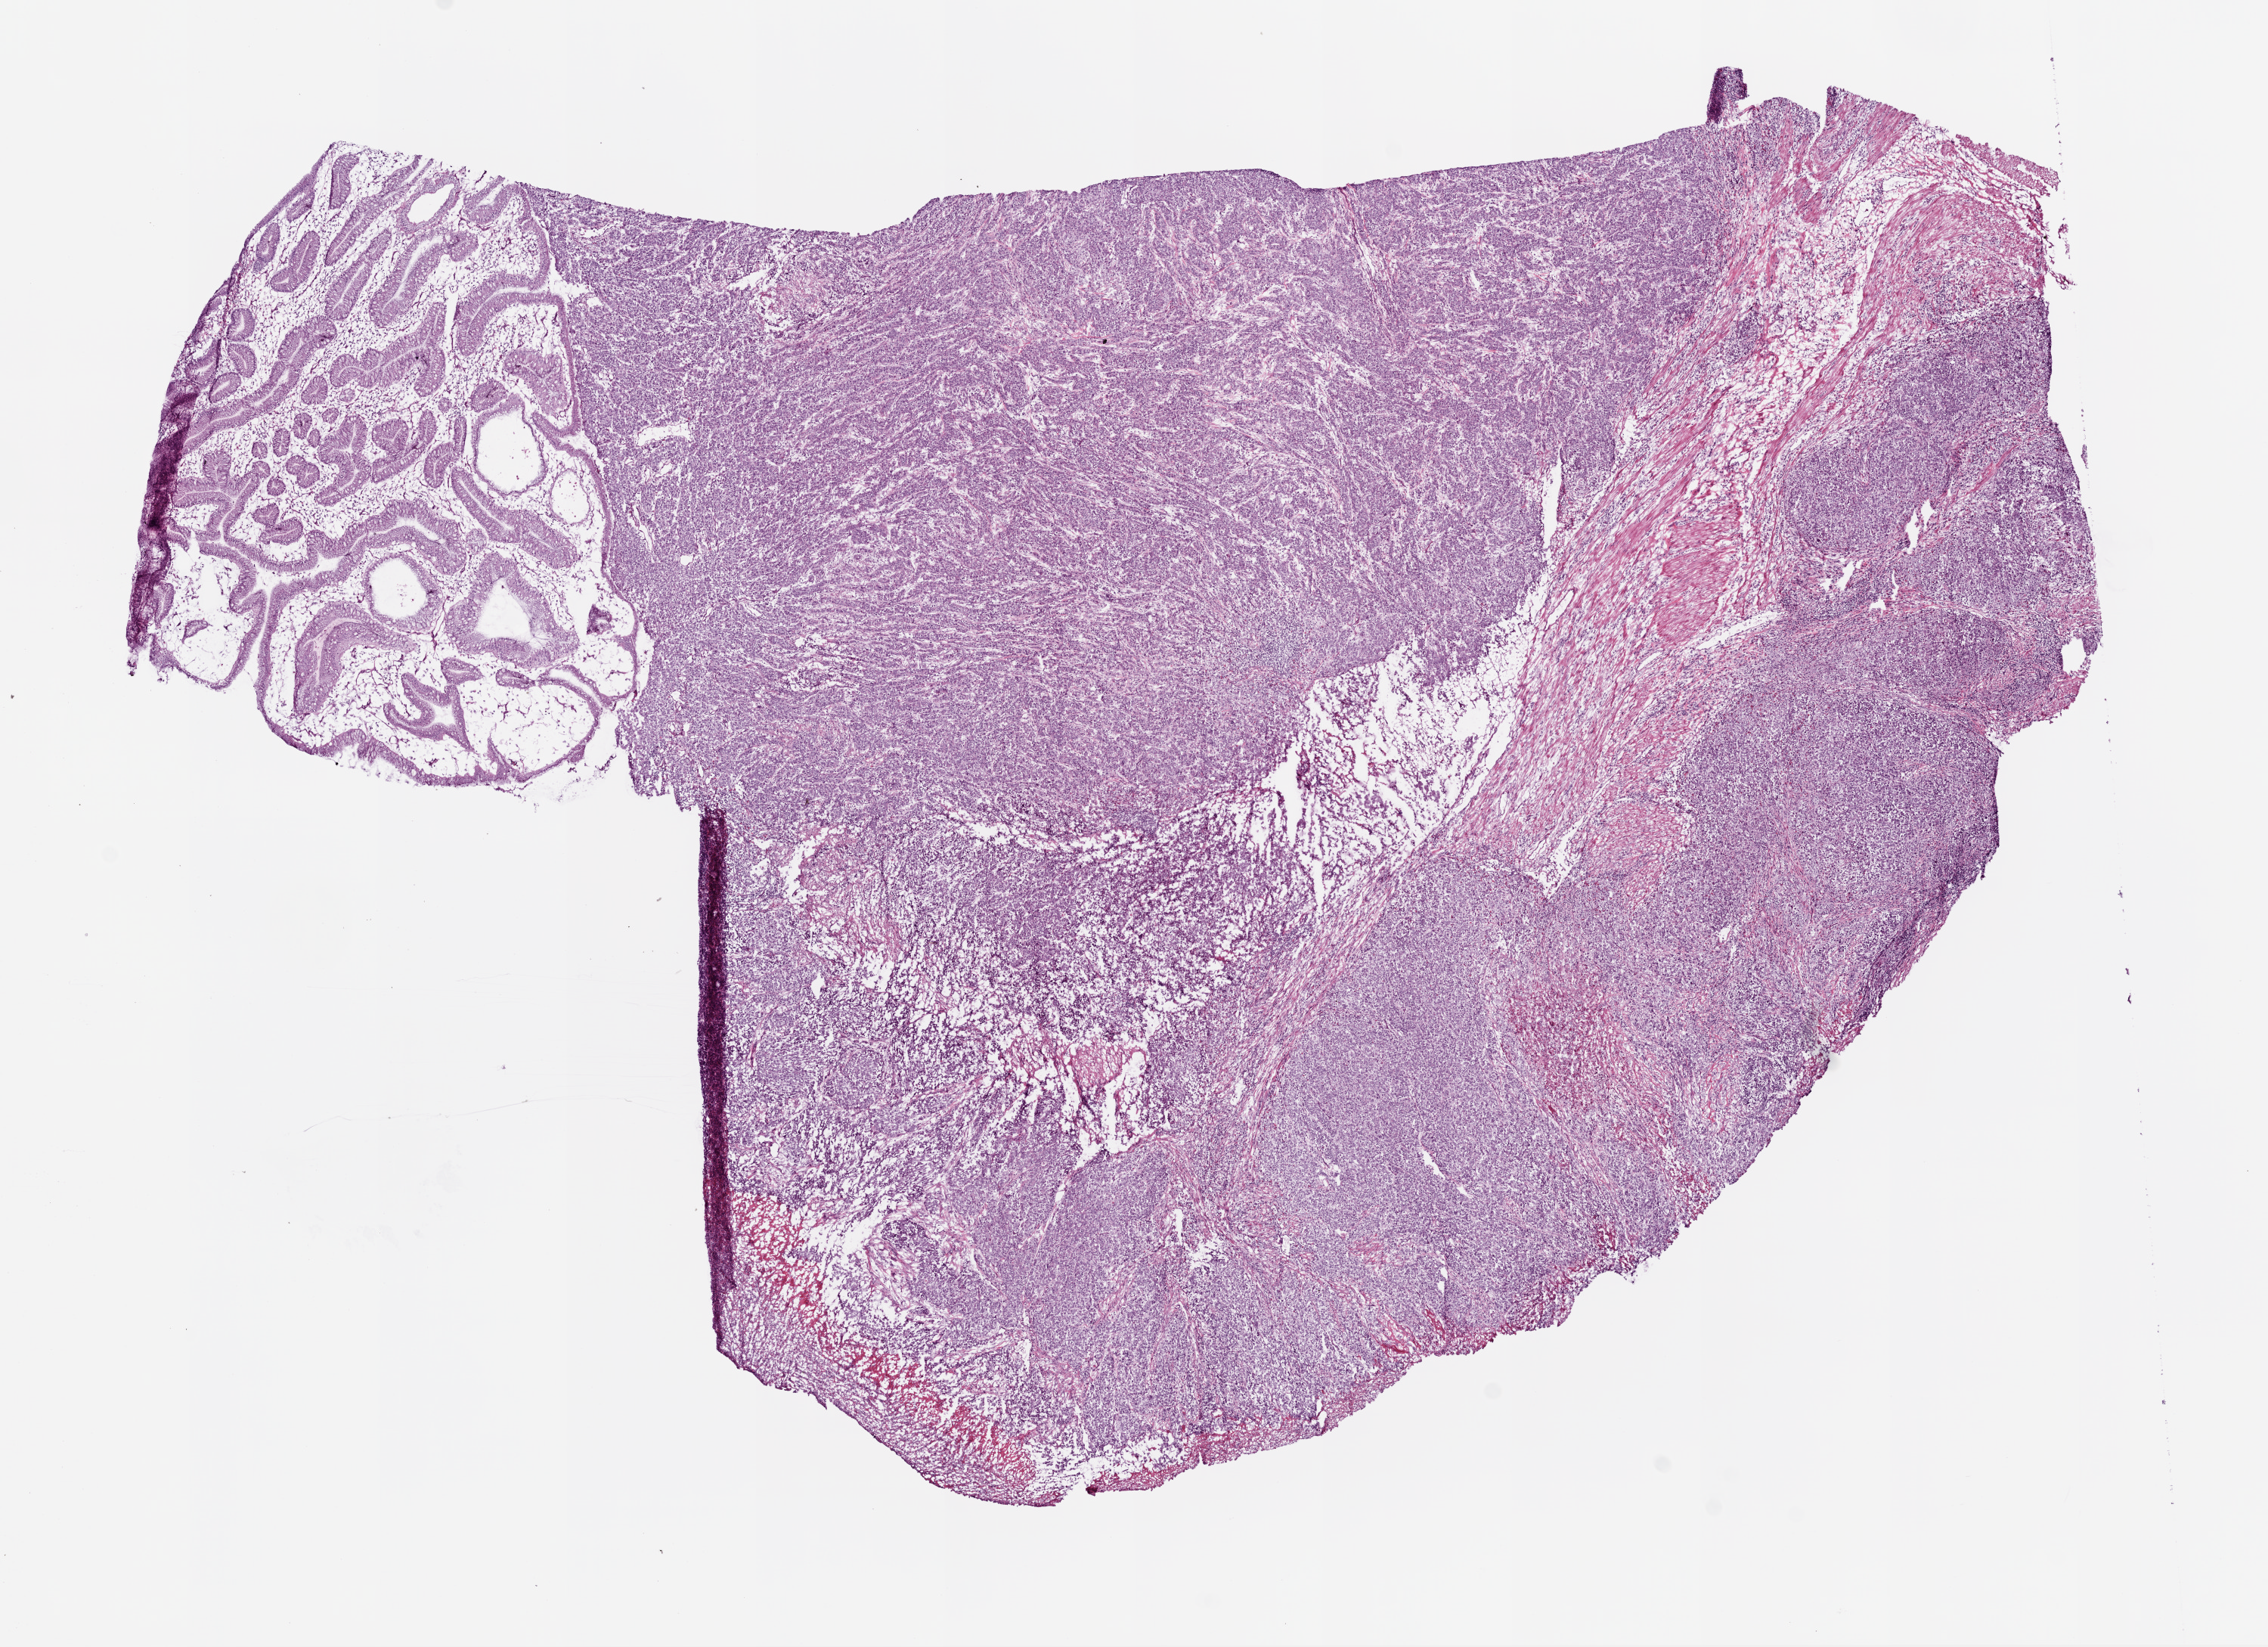
Digitized Hematoxylin and eosin (H&E) stained tissue section (whole slide), a low-resolution overview of the entire scanned area, about 12.0 x 8.7 mm. Frozen section from the bottom of the tissue portion. Primary tumour sample from the stomach. Patient: male, age at initial diagnosis 58 years. Histologic grade: G3 (poorly differentiated). Slide review estimates, as recorded: tumour cells 75%, tumour nuclei 80%, normal cells 10%, stromal cells 12%, necrosis 5%.
AJCC pathologic stage: IV. TNM: T4 N1 M0. Pathologic diagnosis: Adenocarcinoma, intestinal type (gastric antrum).